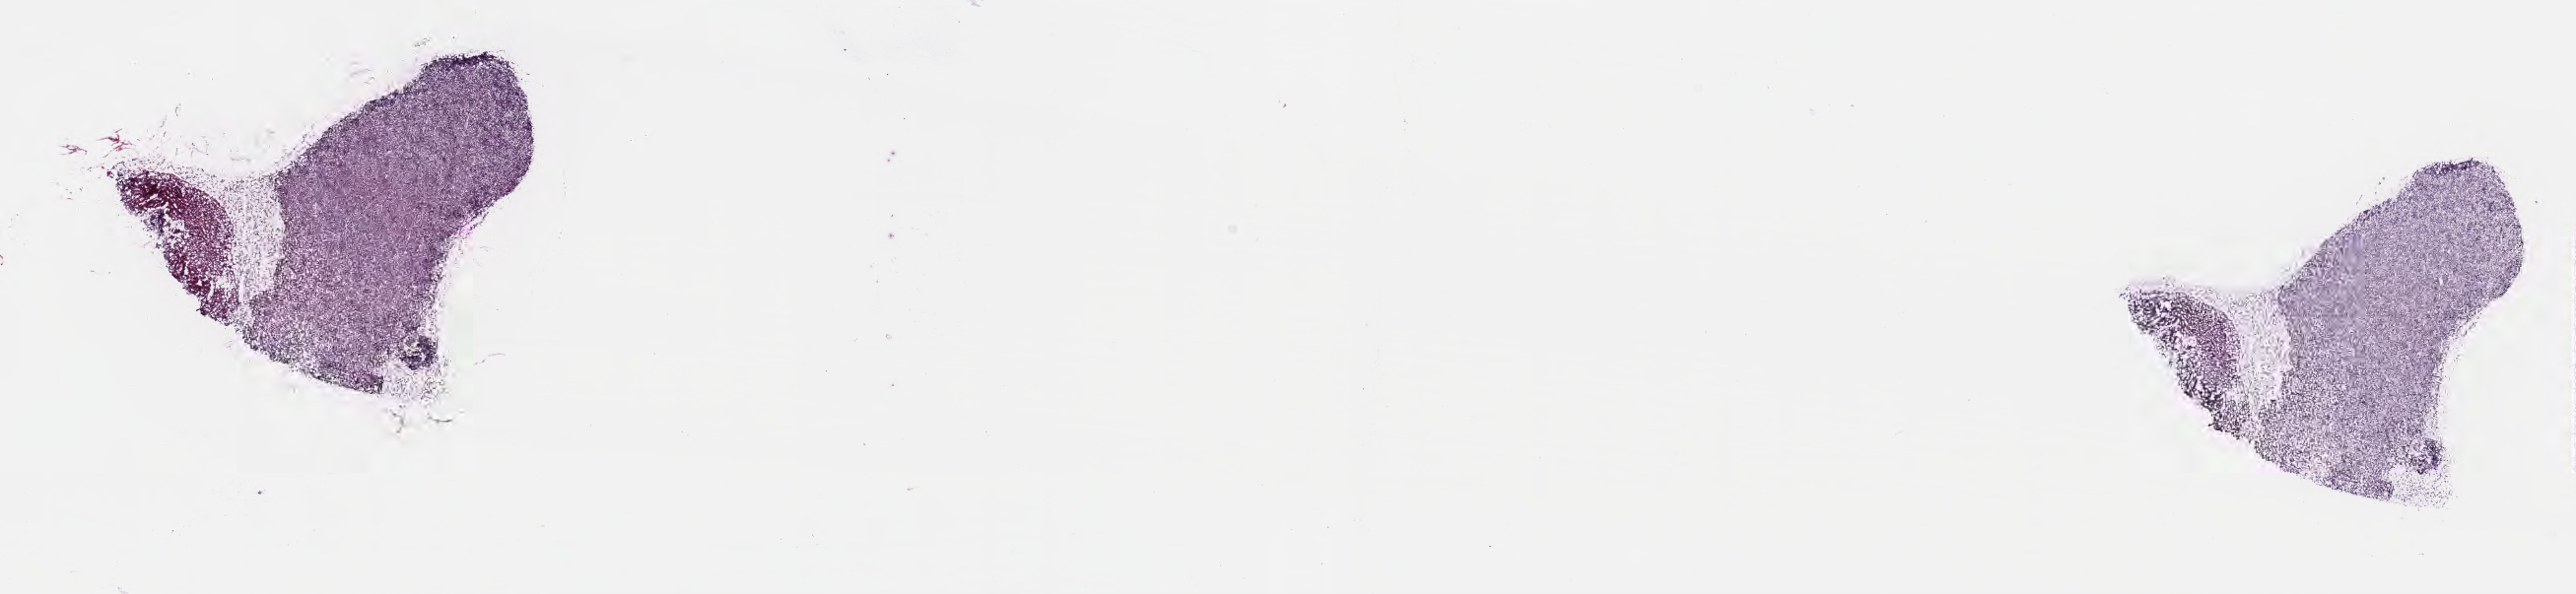
H&E whole-slide image, low-resolution overview of the scanned area, about 21.1 x 4.9 mm, frozen section, primary tumor, site: mandible. Male, age 8 years at initial diagnosis. Composition of this section per pathologist review: tumor cells 80%, tumor nuclei 85%, stromal cells 5%, necrosis 0%, normal cells 15%. Infiltration values recorded for this section: lymphocyte infiltration 70%, monocyte infiltration 15%, neutrophil infiltration 5%.
• Ann Arbor stage (patient): Stage II
• histologic diagnosis: Burkitt lymphoma, NOS
• section: bottom of the tissue portion